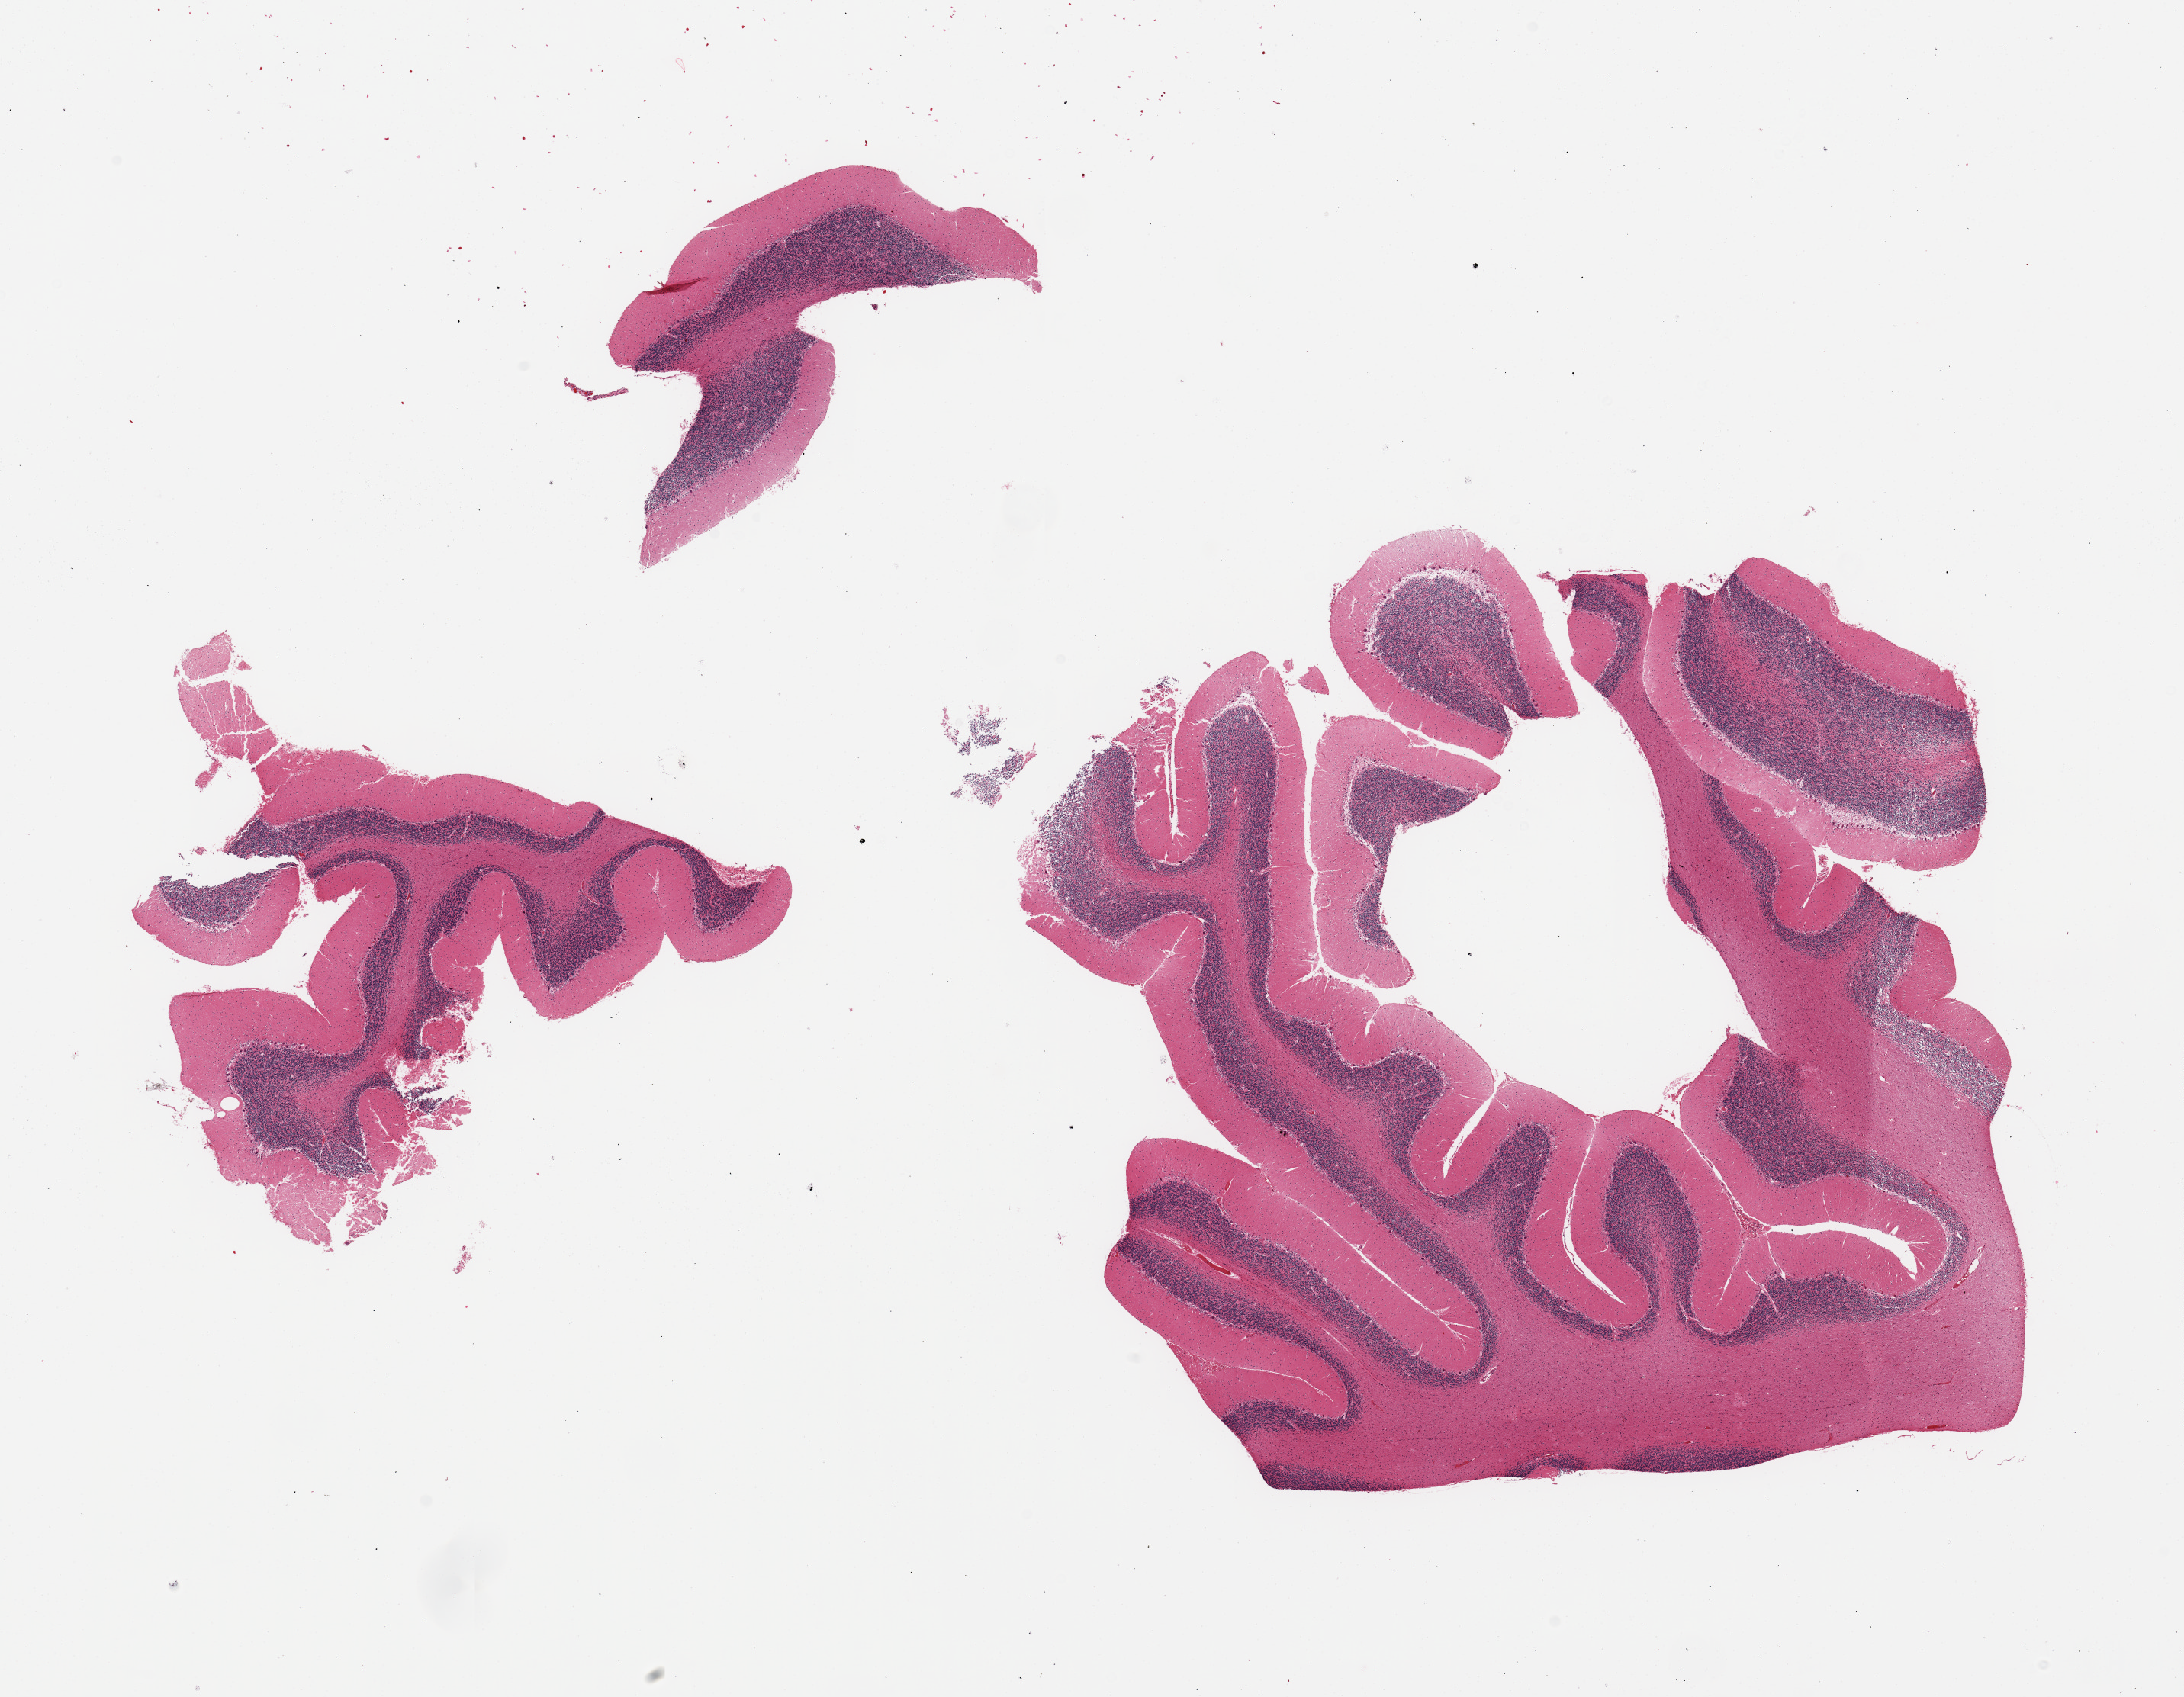
Hematoxylin and eosin (H&E) whole-slide image, brightfield, low-resolution overview of the scanned area, about 22.6 x 17.6 mm; PAXgene-fixed, paraffin-embedded tissue; section of cerebellum (target tissue); donor tissue sample. Donor sex: male.
Reviewer comment on this tissue sample: 3 pieces (fragmented).